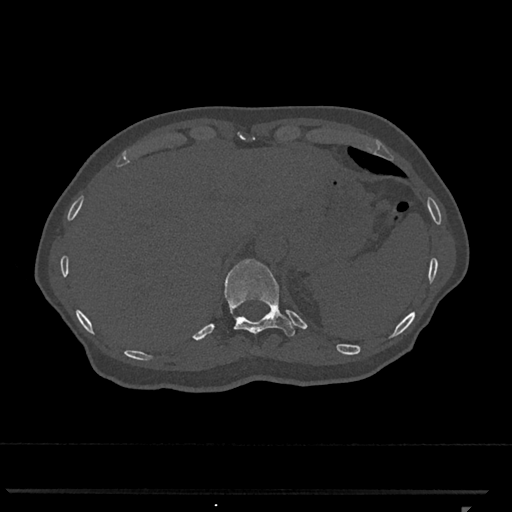
CT including the spine, one axial slice; slice 518 of 793 in the series (ordered by position); reconstruction kernel Br40s/3; bone window (W 1800 / L 400 HU); 0.5 mm slice thickness; 512 × 512 image matrix, field of view 380 × 380 mm. Patient: female, 62 years. From the clinical record (not read from this slice): primary cancer: renal.
Structures marked on this image (semi-automatically segmented with operator editing):
- T11 vertebra: box from (x=224, y=259) to (x=295, y=338) px